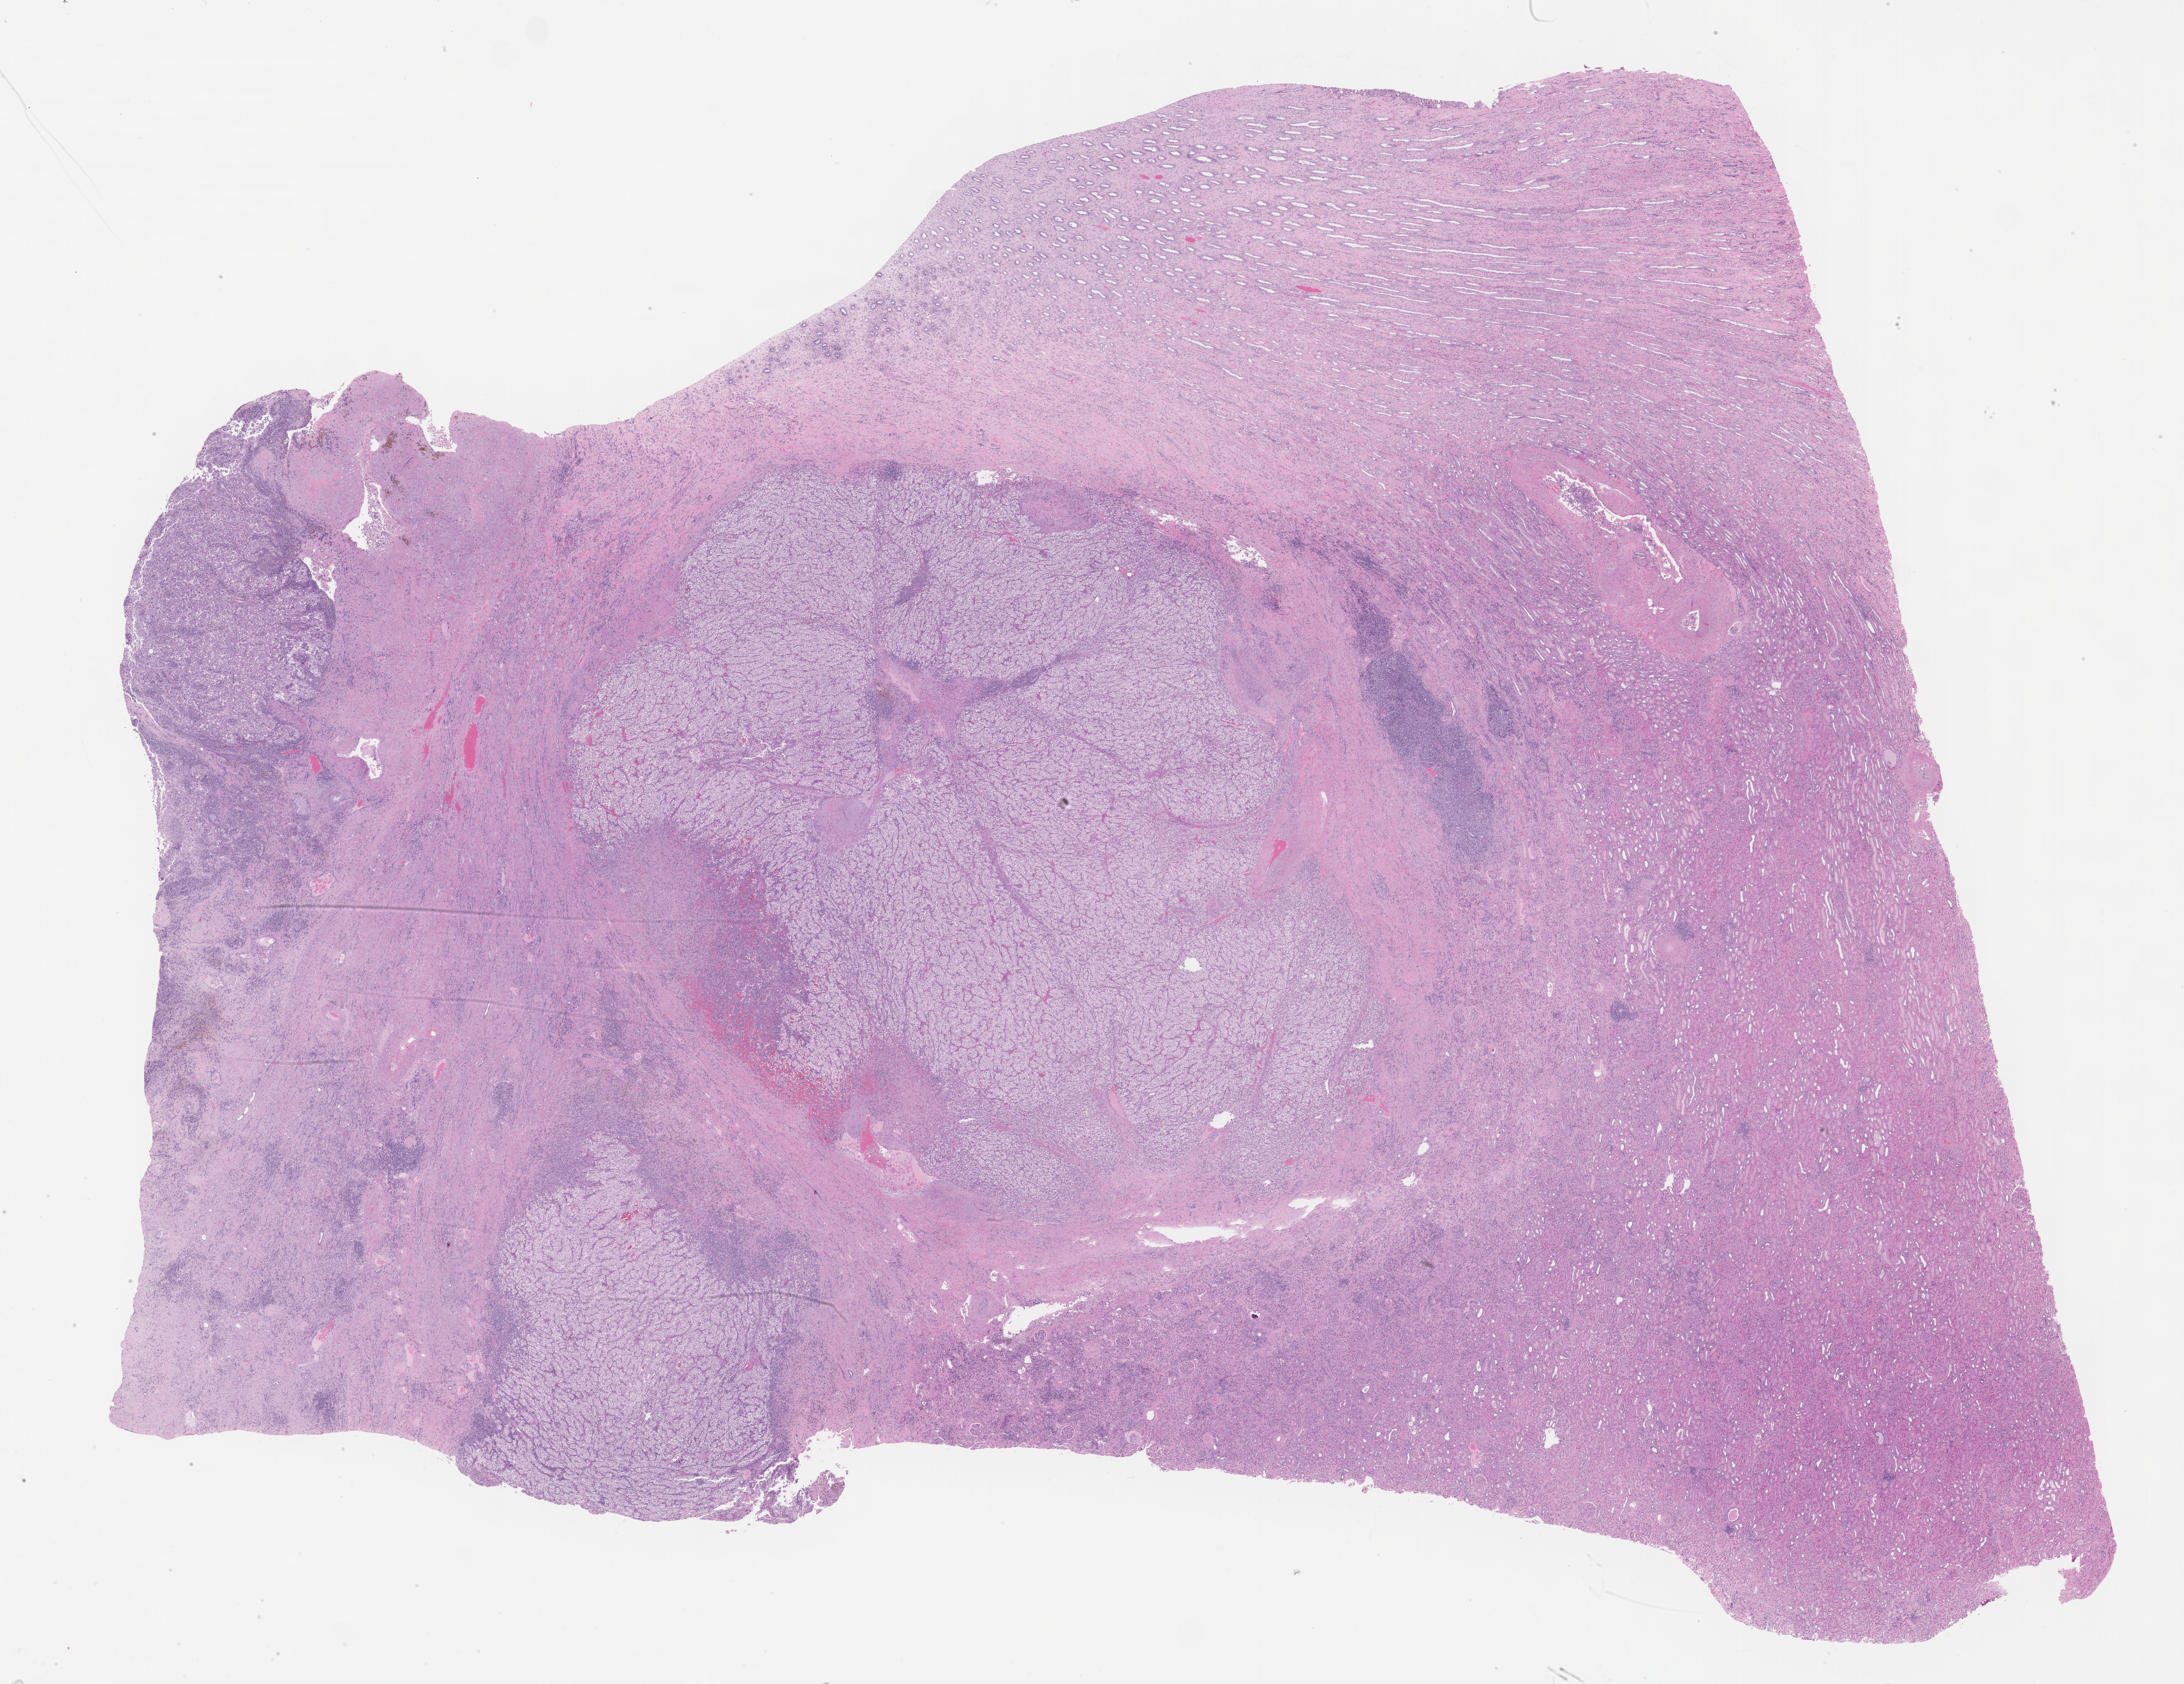
Digitized H&E-stained tissue section (whole slide) — low-resolution overview of the scanned area, about 27.7 x 21.3 mm (slide scanned at 40x), FFPE section, primary tumour sample from the kidney. Male, age 58 years at initial diagnosis.
Diagnosis: Clear cell adenocarcinoma, NOS.